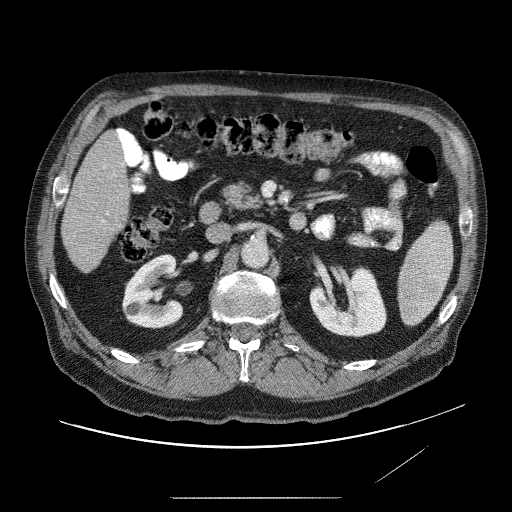
Contrast-enhanced abdominal CT (liver protocol), one axial slice; slice 20 of 89 in the series (ordered by position); reconstruction kernel STANDARD; 120 kVp; soft-tissue window (W 400 / L 40 HU); 512 × 512 image matrix, field of view 420 × 420 mm. Case-level facts recorded for this patient, not image findings: diagnosis: hepatocellular carcinoma (patient treated with transarterial chemoembolisation; whether this scan precedes or follows treatment is not stated here); TNM stage (as recorded): Stage-IVA; Child-Pugh class: A; tumour differentiation: moderately differentiated.
Annotated regions visible in this slice (semi-automatic segmentation, software-assisted and operator-edited):
- liver parenchyma outside the tumour (the mass and vessels are separate outlines, so this box may not span the whole liver): bounding box [x1, y1, x2, y2] px = [60, 122, 136, 274]
- liver vessels: [97, 128, 129, 244]